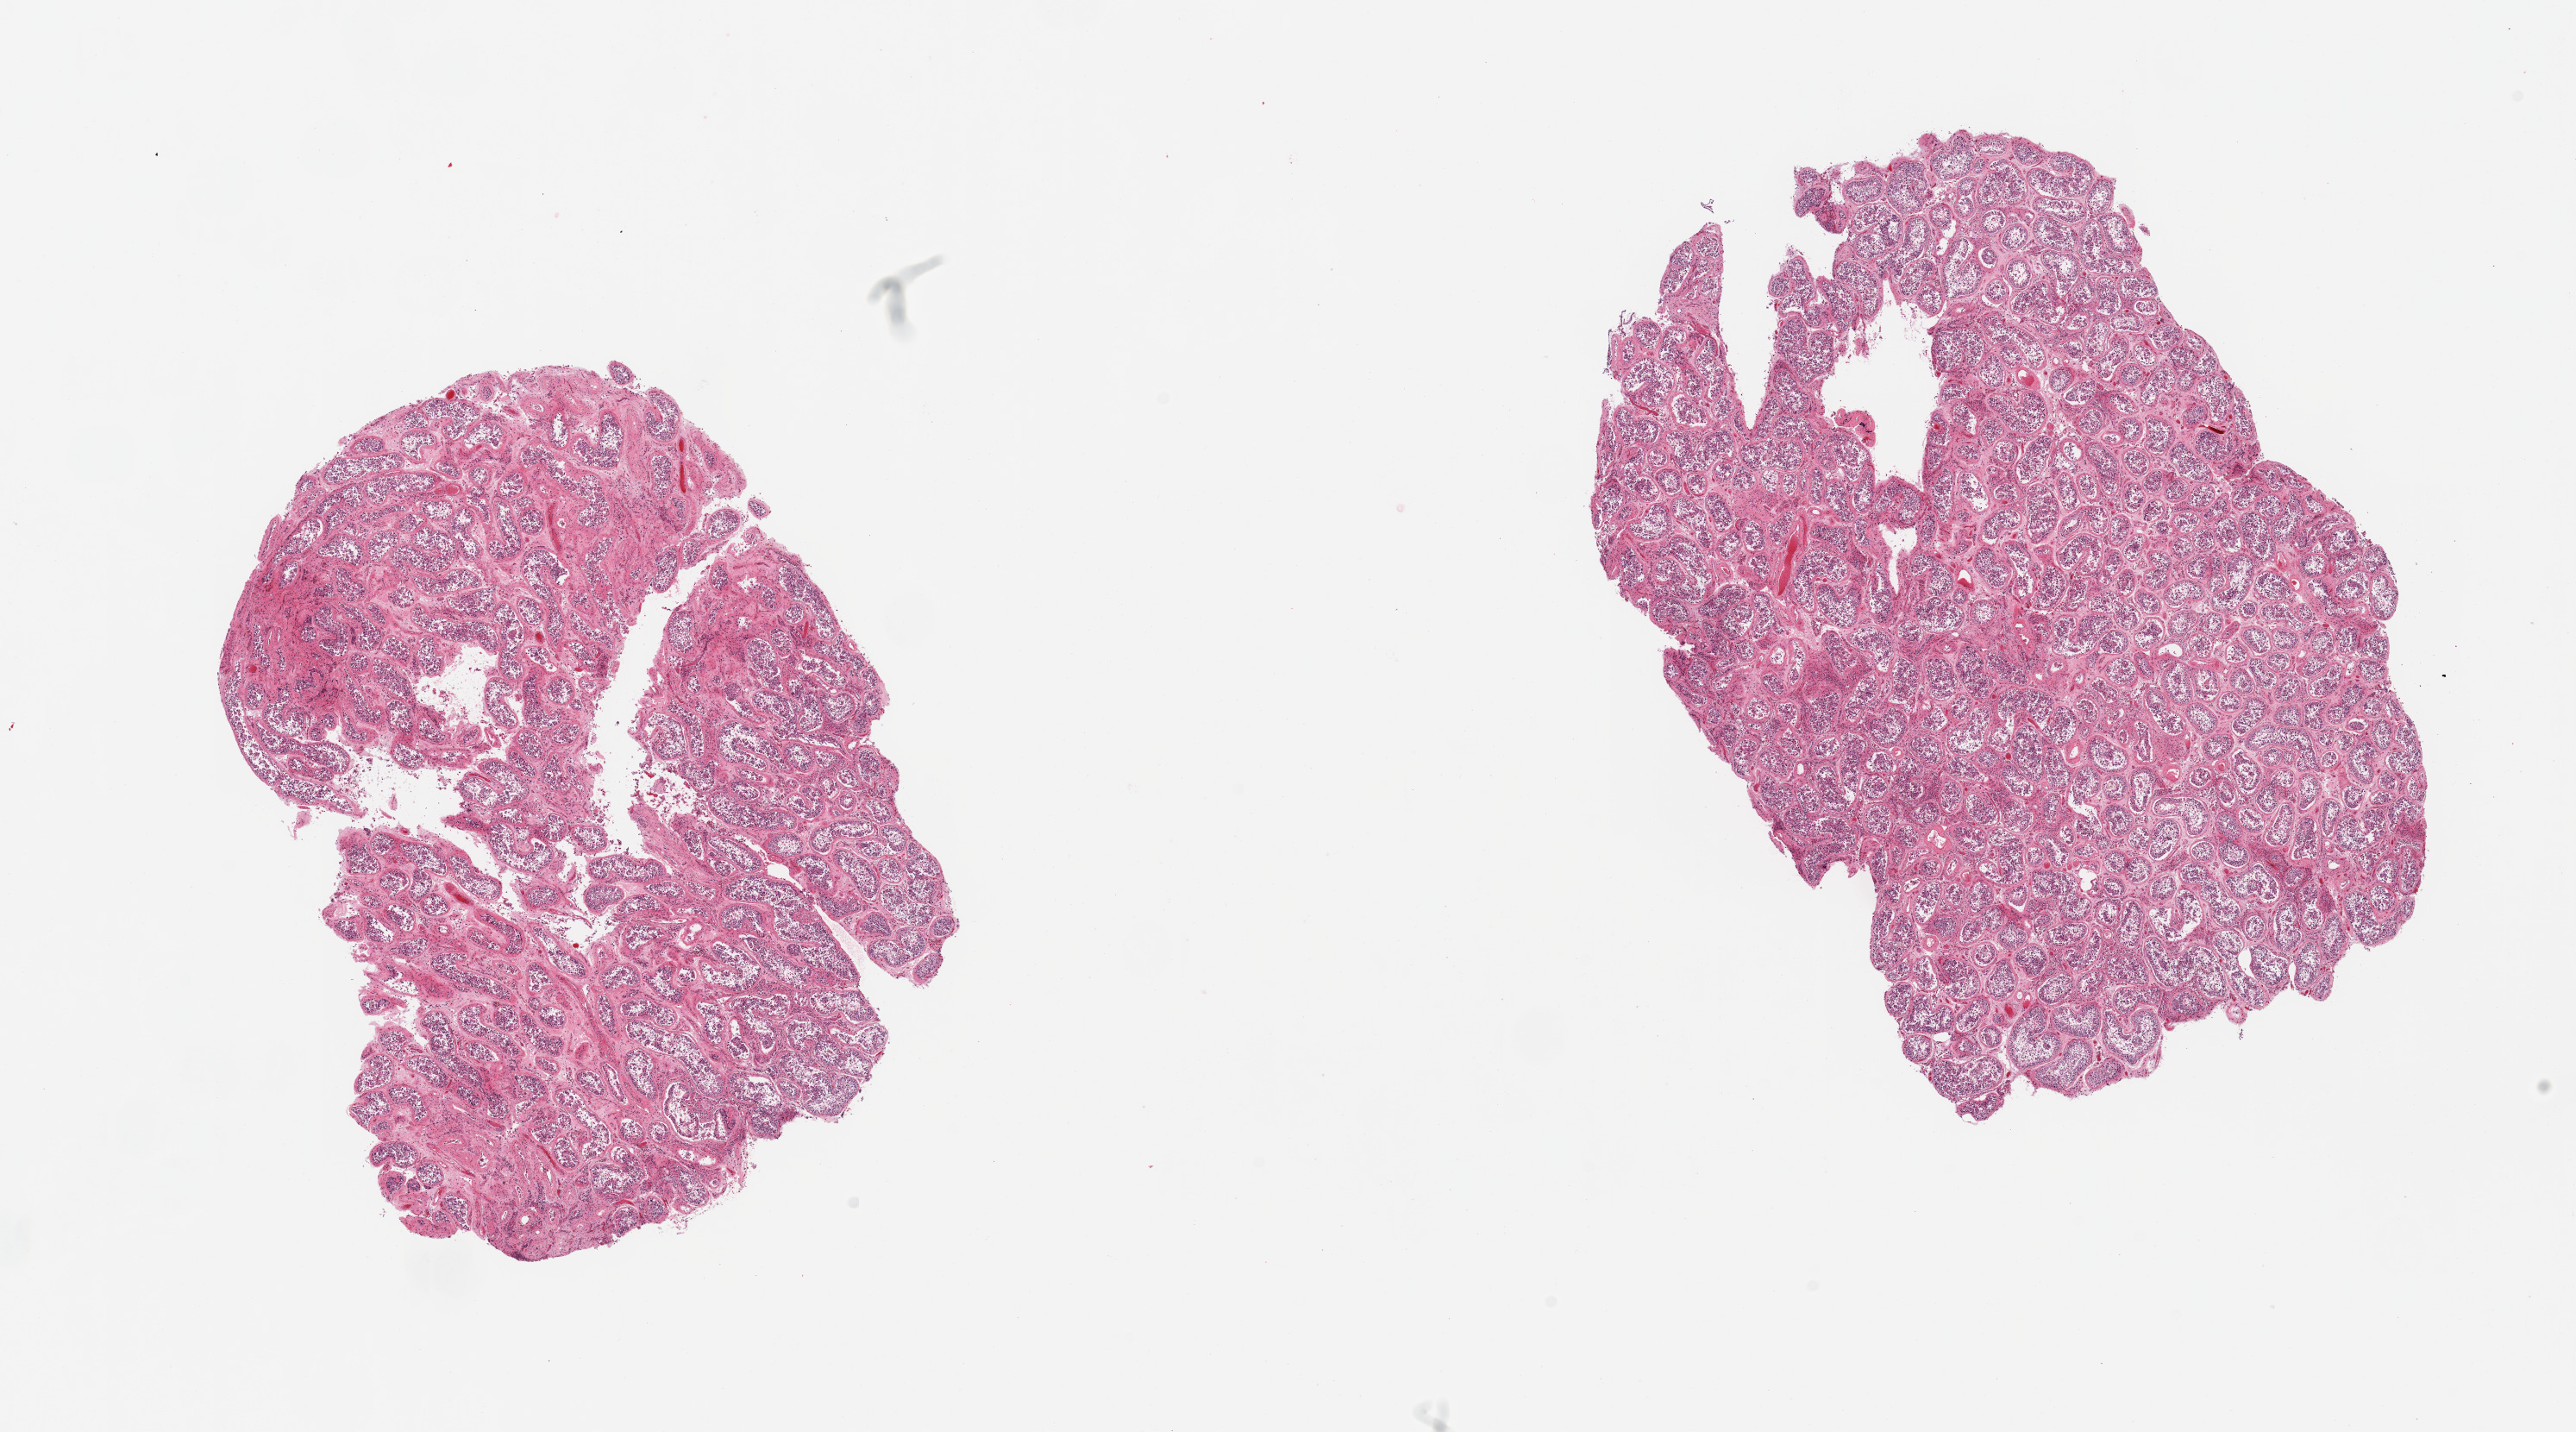
Whole-slide image, H&E stain, whole scanned area (about 23.6 x 13.1 mm) shown as a low-resolution overview, PAXgene-fixed, paraffin-embedded tissue, sampled site (target tissue): testis, tissue donor sample. Male donor.
Reviewer comment on this tissue sample: 2 pieces; spermatogenesis is present, few hyalinized tubules.